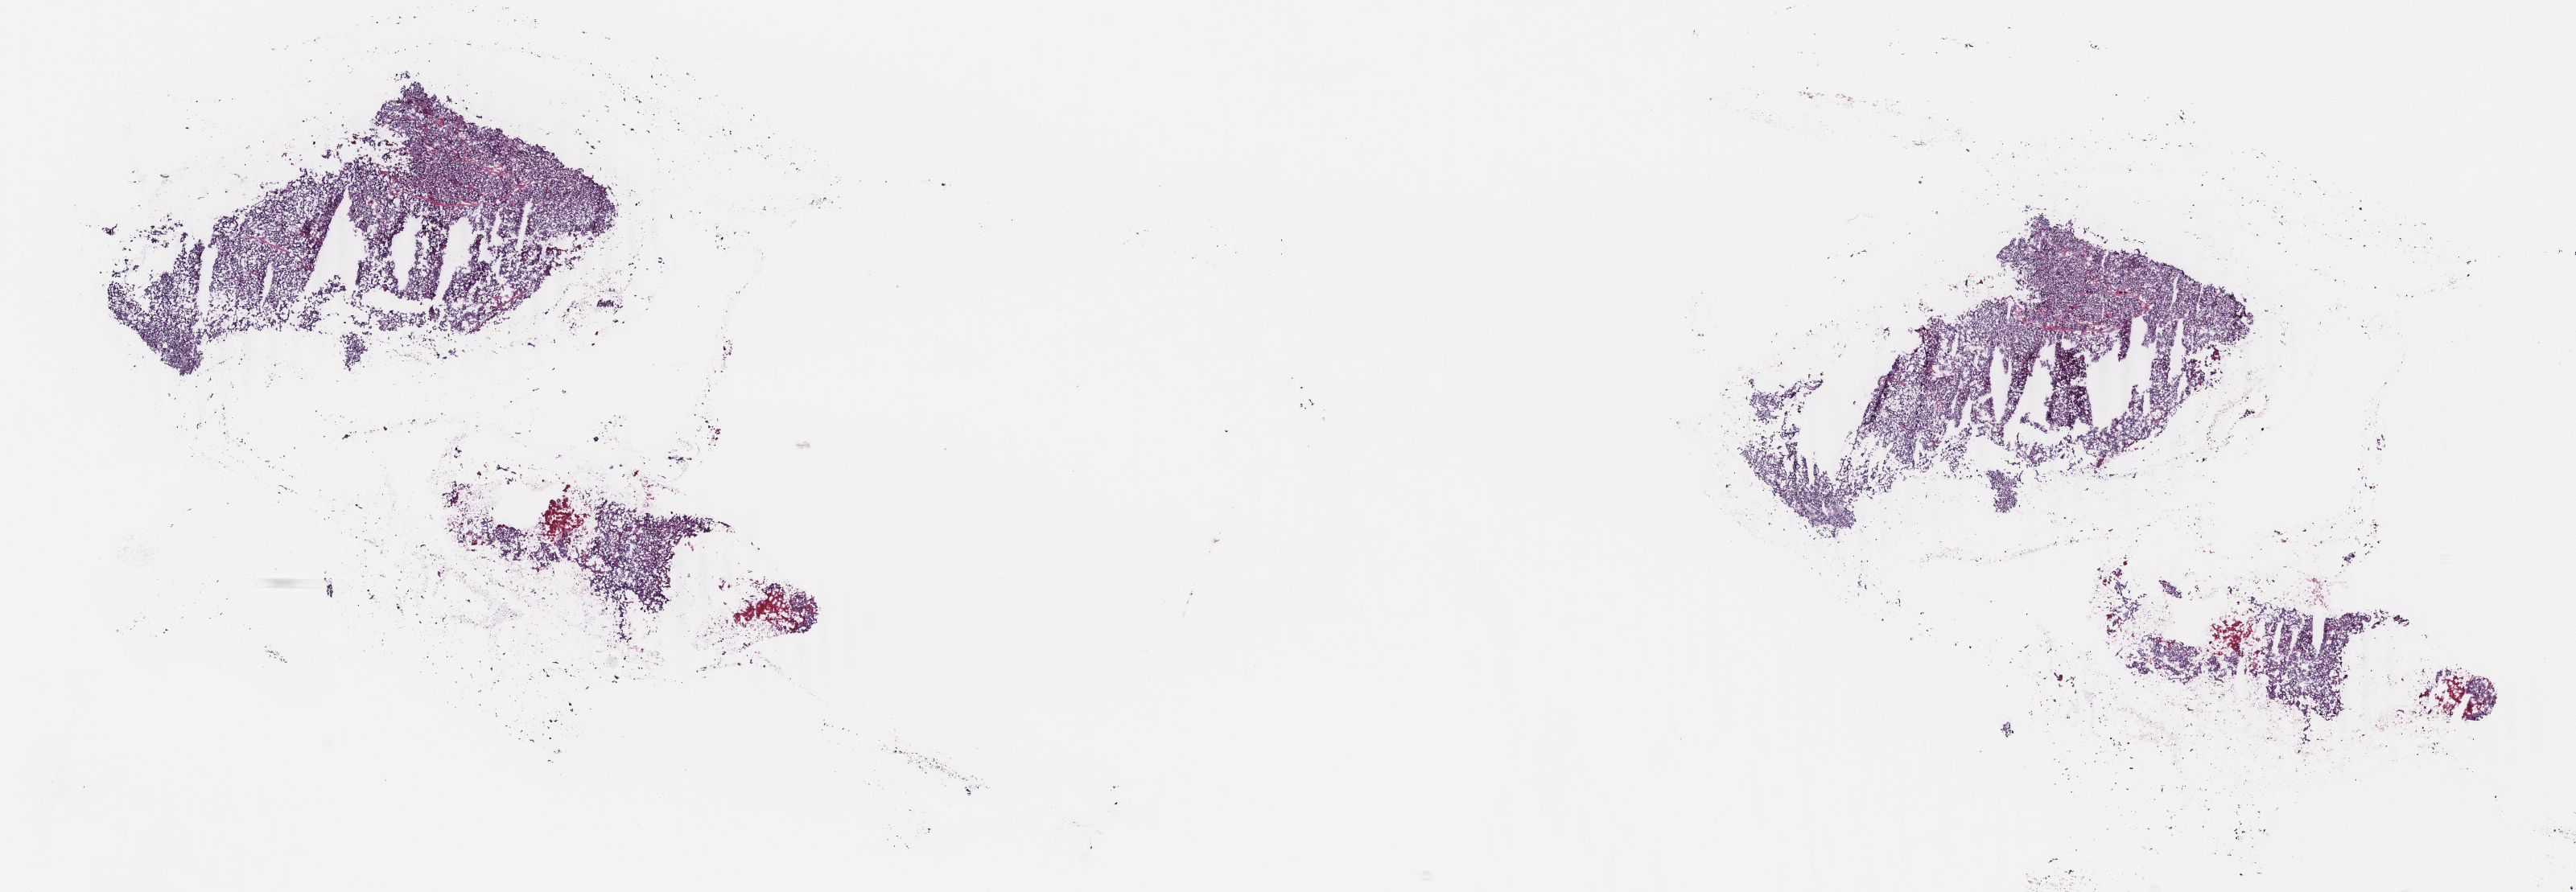
Digitized H&E tissue section (whole slide) — low-resolution overview of the scanned area, about 25.5 x 8.8 mm (from a 40x scan). Frozen section from the top of the tissue portion. Primary tumour sample from the adrenal gland. Patient: female, age at initial diagnosis 19 years. Composition of this section per pathologist review: tumour cells 99%, tumour nuclei 99%.
Pathologic diagnosis: Medullary carcinoma, NOS (thyroid gland).